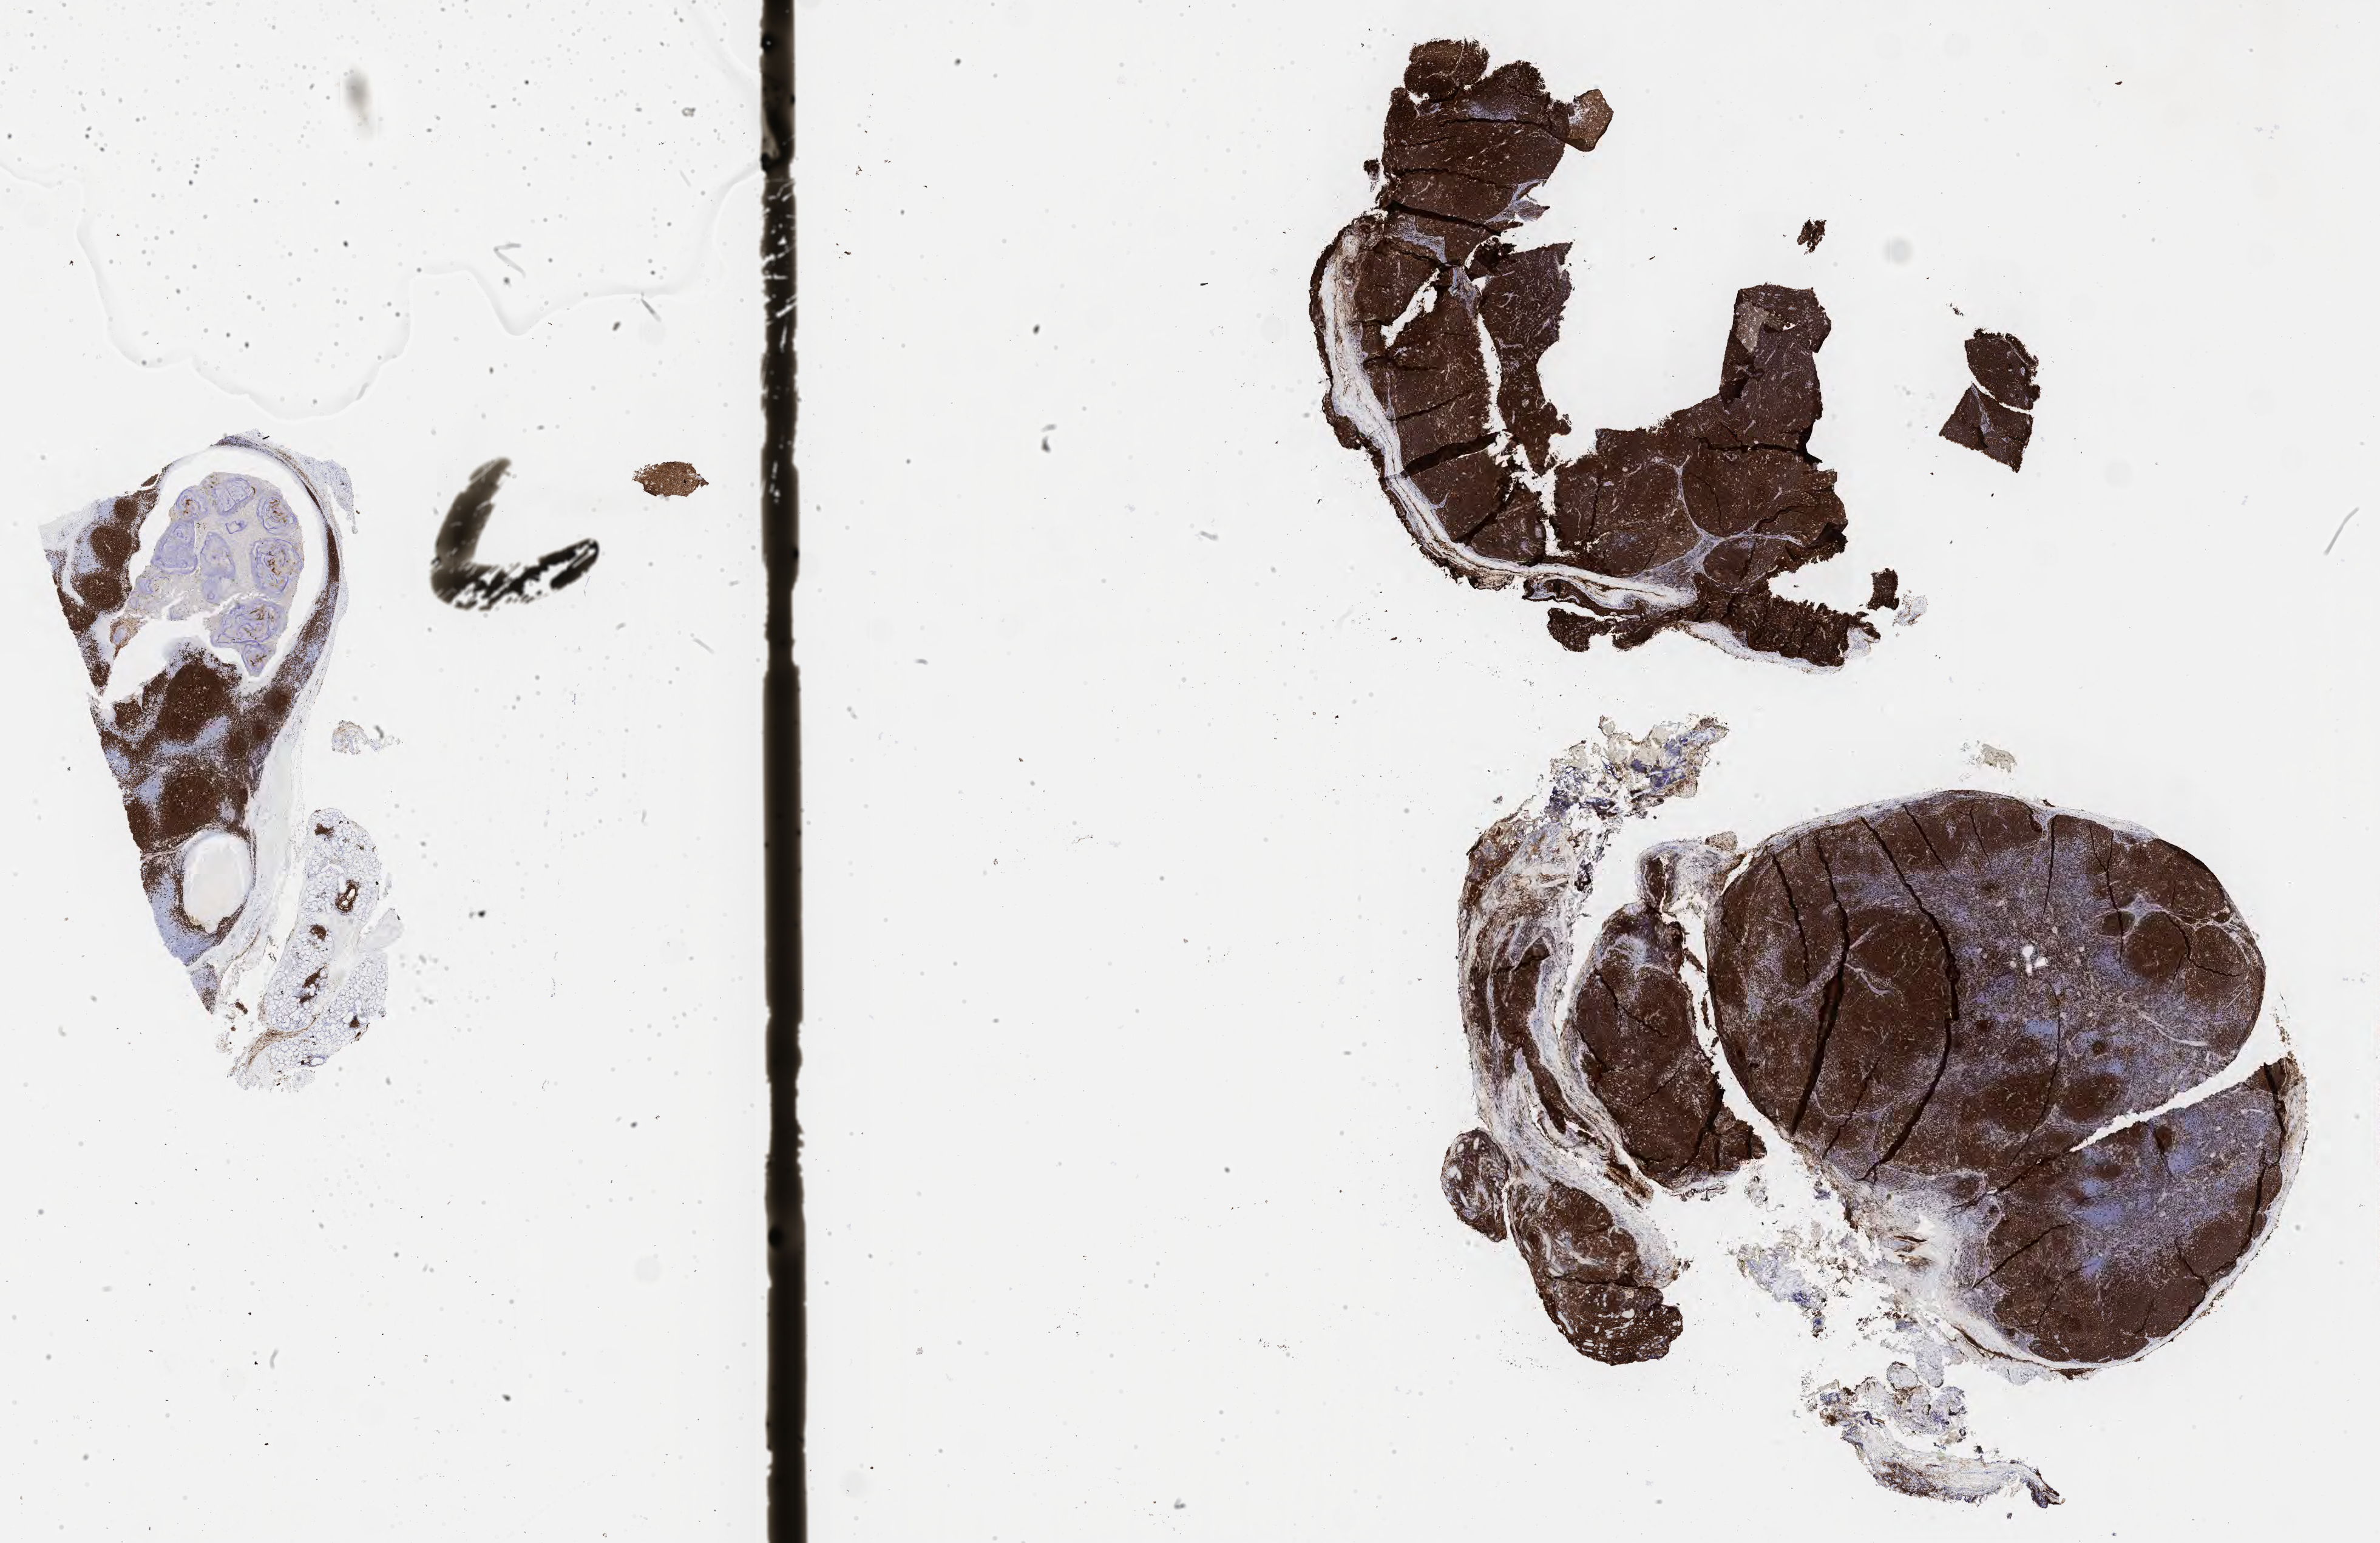
IHC for CD20, whole-slide image — low-resolution overview of the scanned area, about 31.7 x 20.6 mm; tumor tissue. Male patient, age 25 years.
• histologic diagnosis: Burkitt lymphoma, NOS